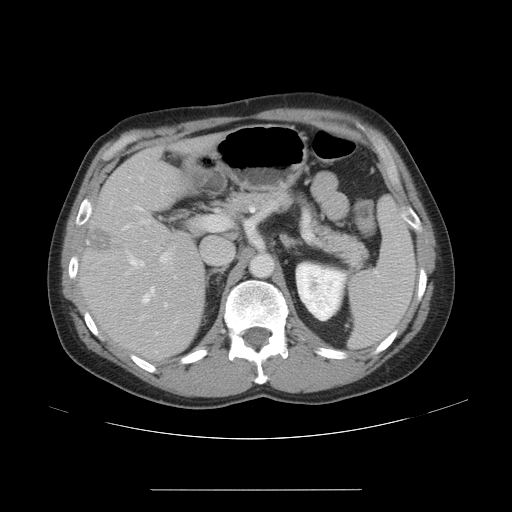
Contrast-enhanced abdominal CT, one axial slice; position 28 of 48 along the scan axis; reconstruction kernel STANDARD; 120 kVp; soft-tissue window (W 400 / L 40 HU); 5 mm slice thickness; 512 × 512 image matrix, field of view 409 × 409 mm. Male patient, age 56 years. From the clinical record (not read from this slice): diagnosis: colorectal cancer liver metastases, imaged before liver resection.
Annotated regions visible in this slice (outlined manually by an expert reader):
- hepatic veins: bounding box [x1, y1, x2, y2] px = [125, 176, 164, 305]
- liver: [82, 140, 207, 356]
- planned liver remnant (the part of the liver to remain after resection): [84, 140, 207, 357]
- portal vein (with intrahepatic branches): [122, 188, 221, 307]
- liver metastasis: [86, 227, 112, 254]